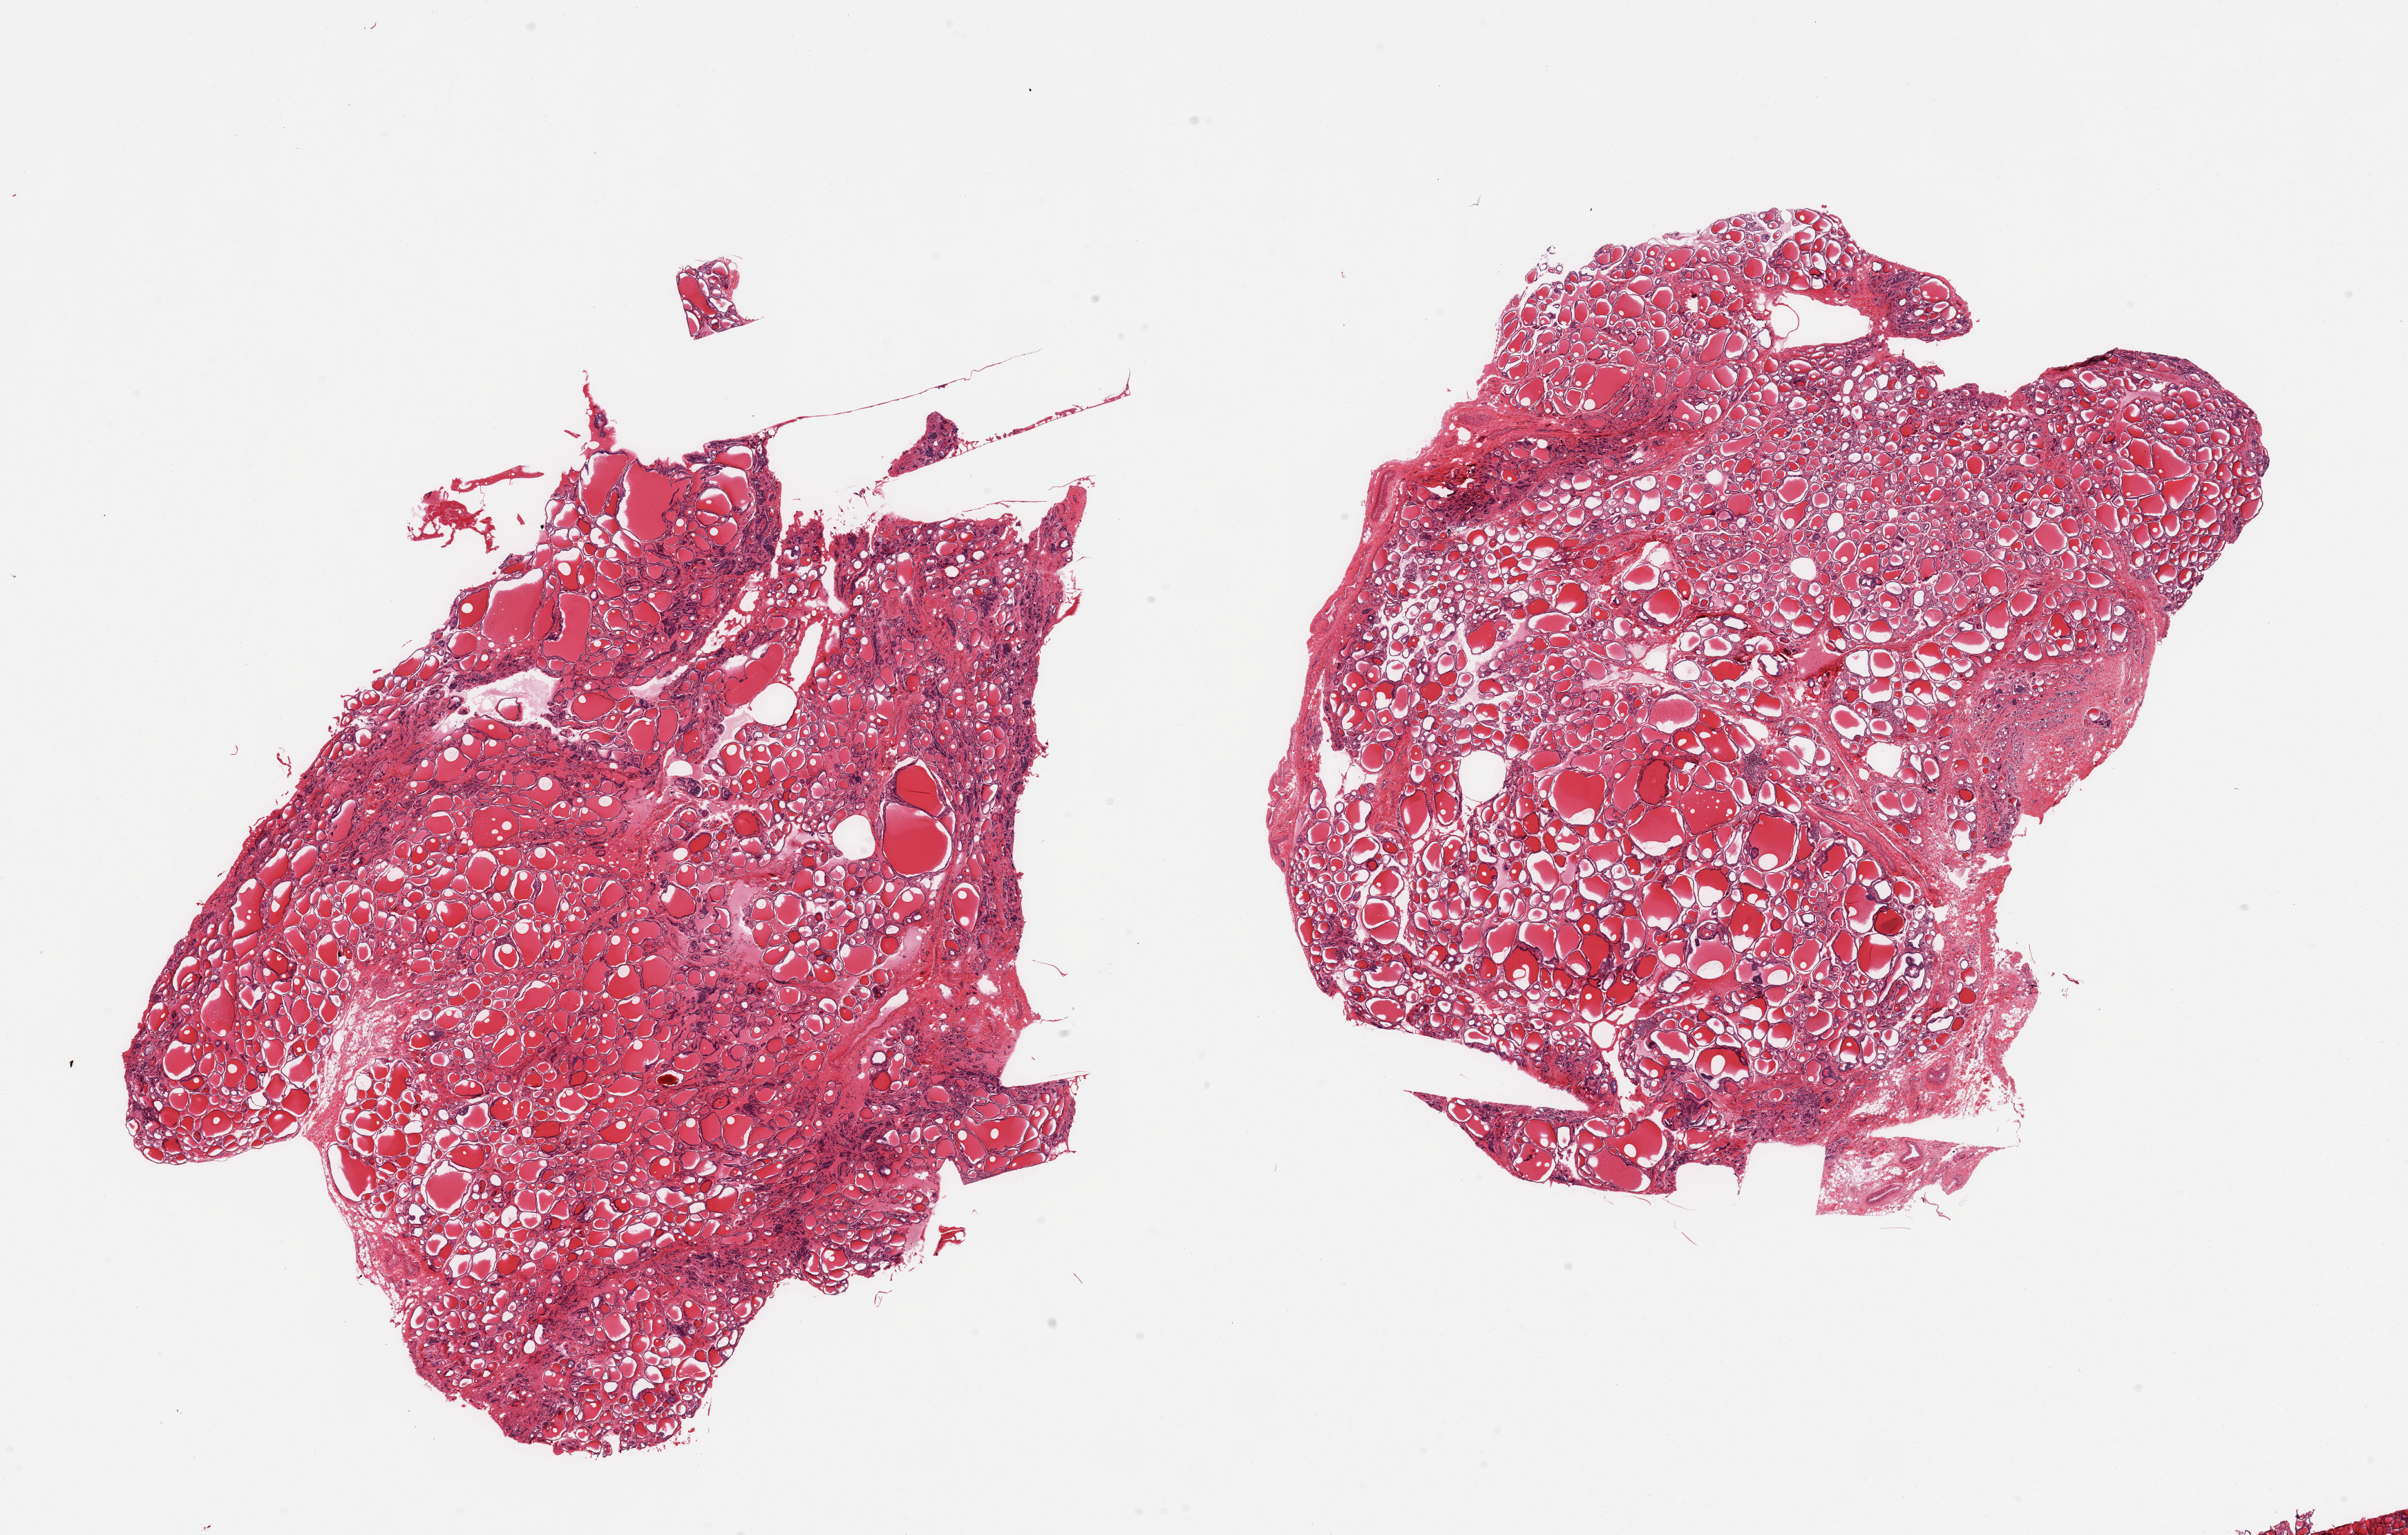
H&E whole-slide image, a low-resolution overview of the entire scanned area, about 27.6 x 17.6 mm (from a 20x scan), PAXgene-fixed paraffin-embedded (PFPE) section, sampled site (target tissue): thyroid, tissue donor sample. Donor: female.
Pathologist's review note for this sample: 2 pieces; accentuation of interstitial fibrosis with focal scarring.